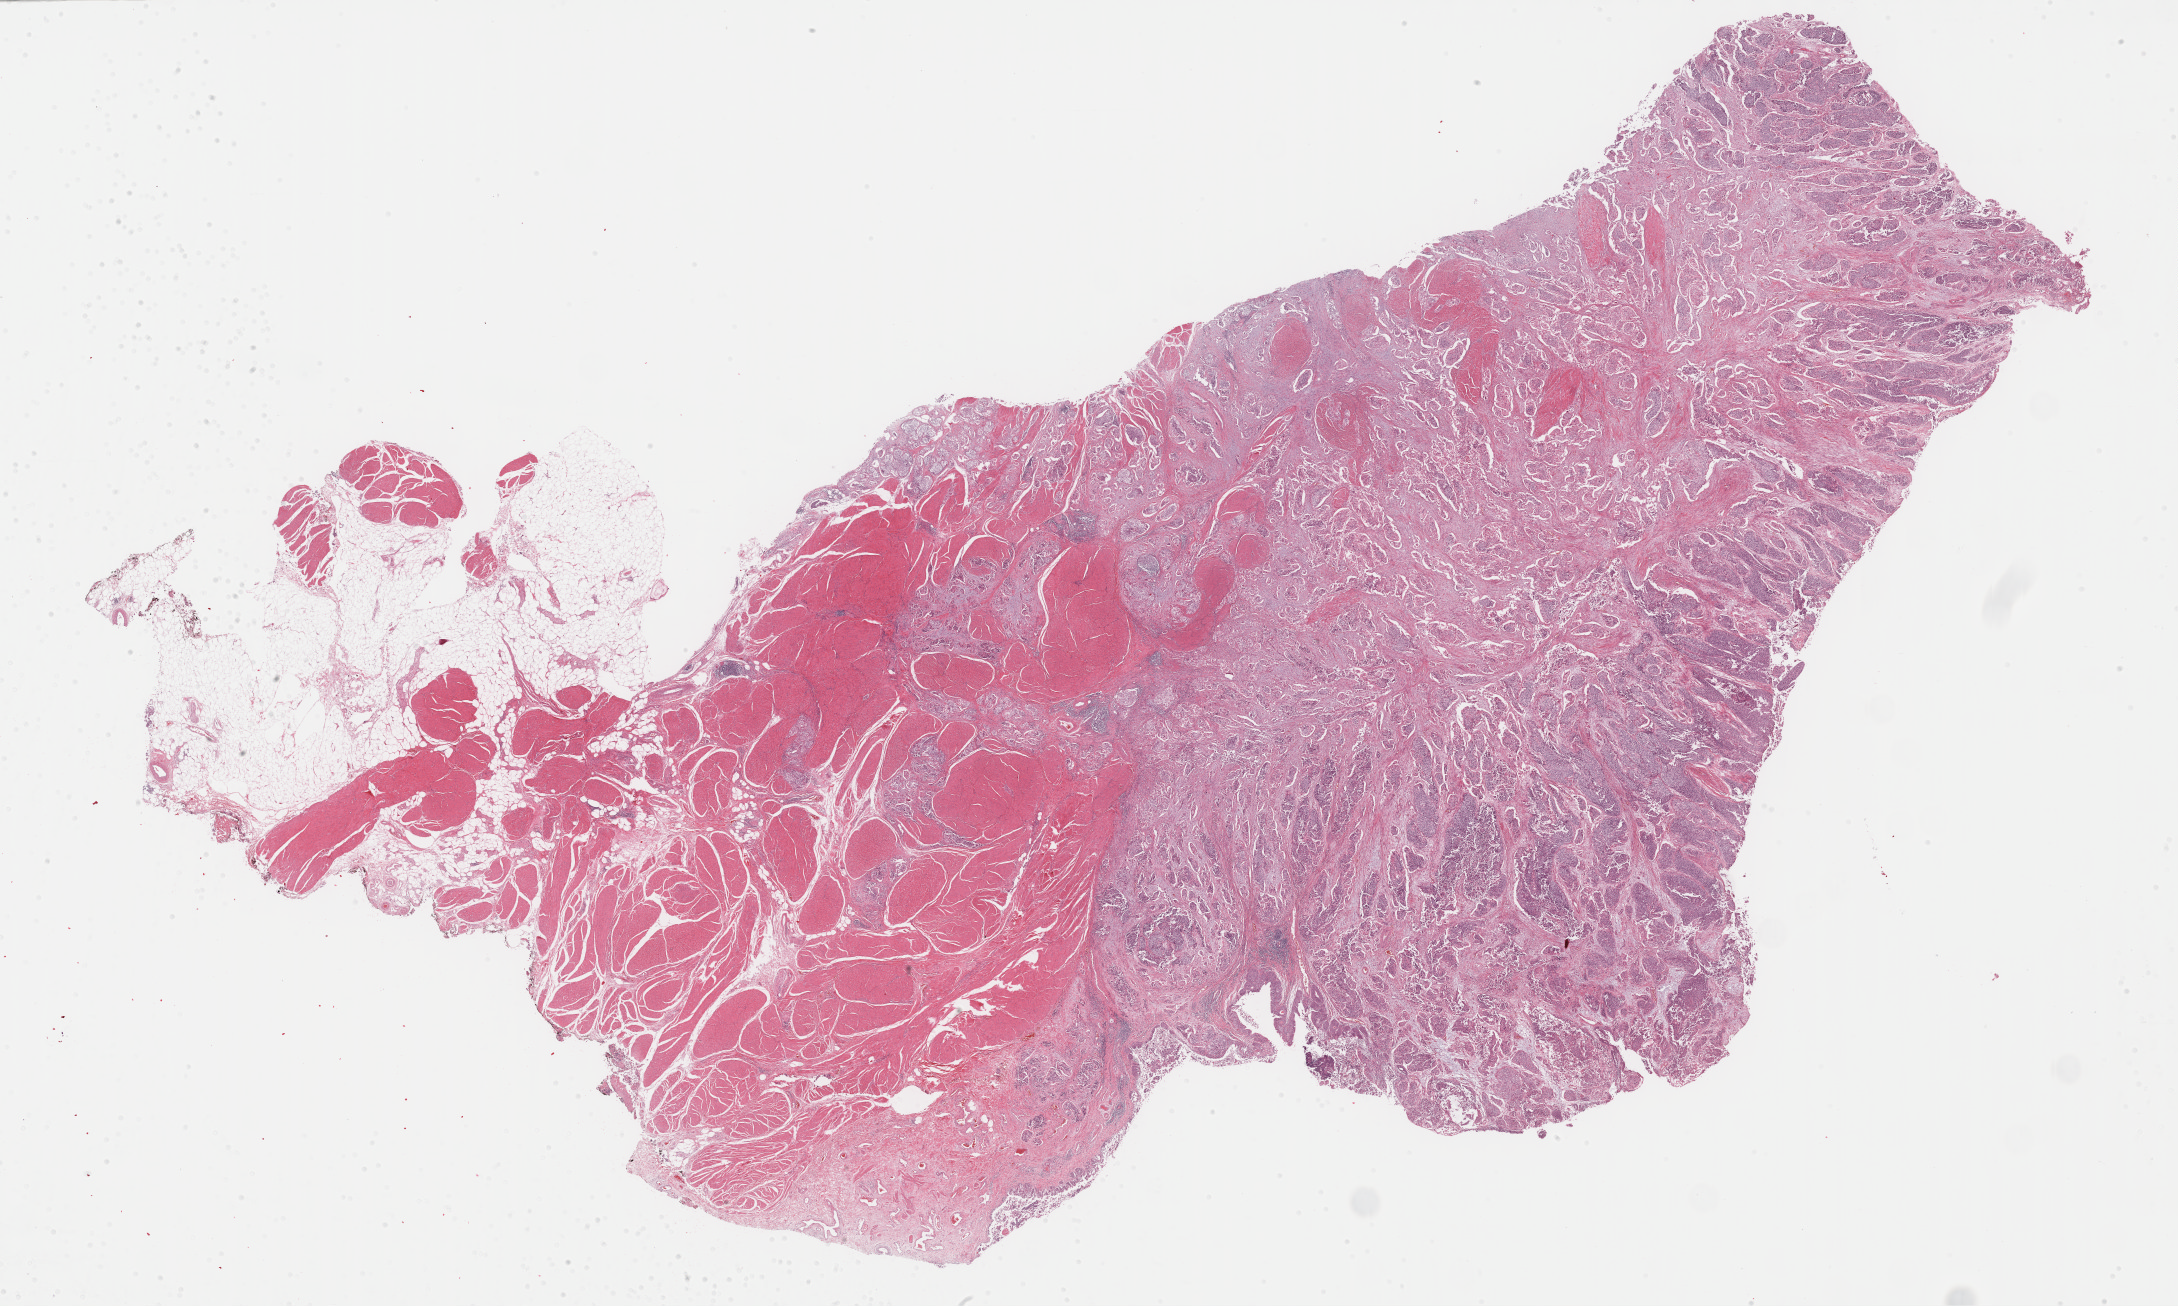
Digitized H&E-stained tissue section (whole slide), whole scanned area (about 35.2 x 21.1 mm, acquisition: 40x scan) shown as a low-resolution overview; formalin-fixed paraffin-embedded (FFPE) diagnostic section; primary tumour sample from the bladder. Patient: male, age at initial diagnosis 69 years. Histologic grade: high grade.
AJCC pathologic stage: III (6th edition). Pathologic diagnosis: Transitional cell carcinoma.